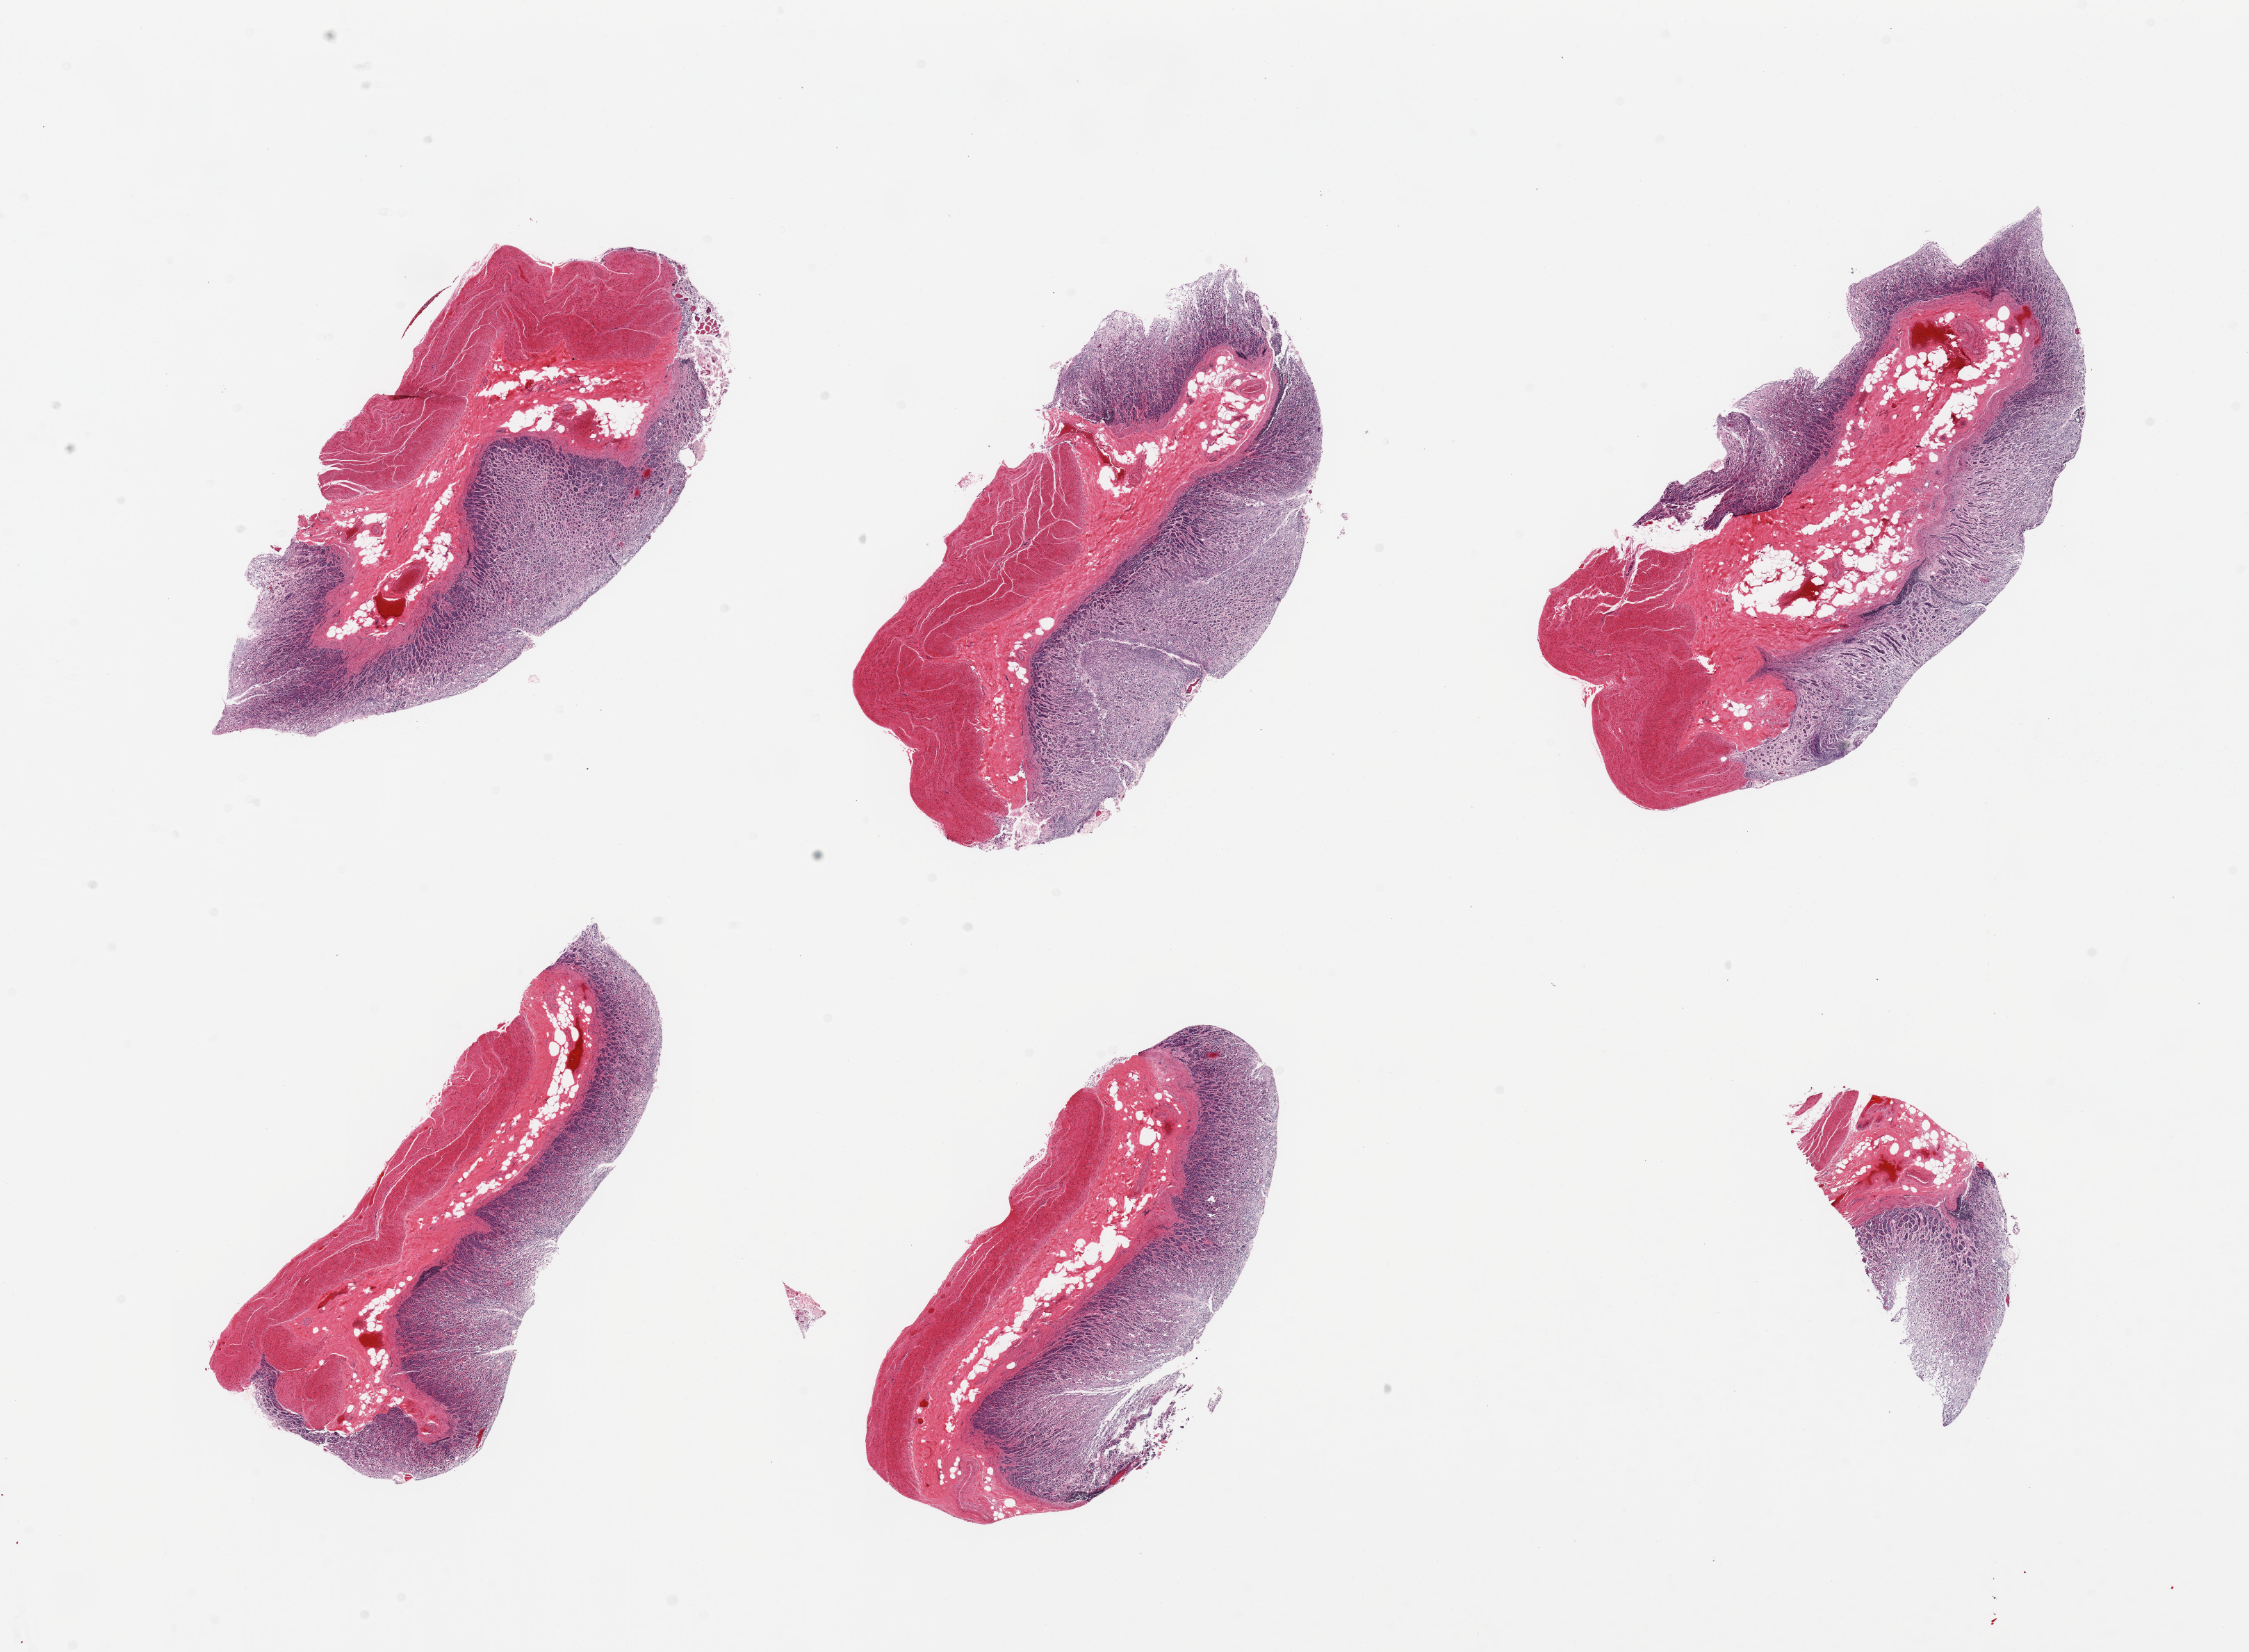
Whole-slide image, haematoxylin and eosin stain, shown as a low-resolution overview of the whole scanned area (about 25.6 x 18.8 mm, from a 20x scan), PAXgene-fixed, paraffin-embedded tissue, sampled site (target tissue): stomach, donor tissue sample. Donor: male.
- pathologist's review note for this sample: 6 pieces; mucosa severely autolyzed, muscularis only slightly autolyzed